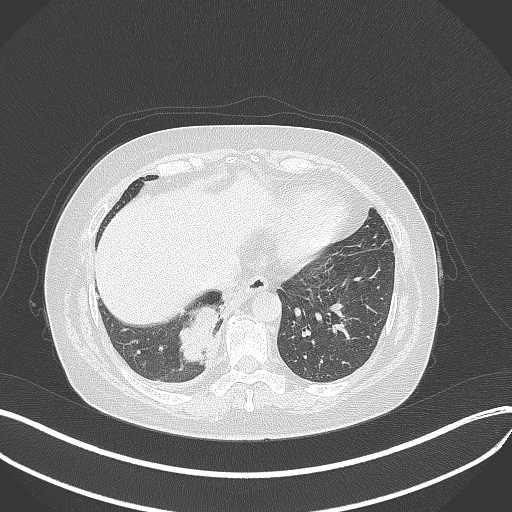
Chest CT, one axial slice. Slice 99 of 381 in the series (ordered by position). Reconstruction kernel B70f. 120 kVp. Lung window (W 1500 / L -600 HU). 1 mm slice thickness. 512 × 512 image matrix, field of view 400 × 400 mm. Female patient, age 56 years. Case-level facts recorded for this patient, not image findings: clinical TNM (as recorded): T2b N1 M0; histopathological grade: G3.
Annotated regions visible in this slice (rectangle marked by the reading radiologist):
- lung tumour (recorded histology: small cell carcinoma): bounding box <177,299,224,368> (left, top, right, bottom; pixels)